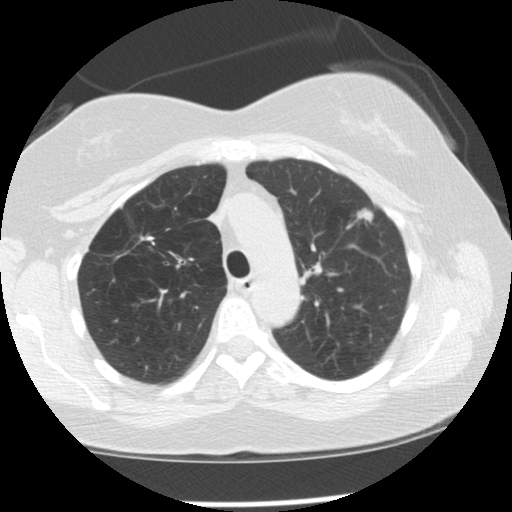
Axial slice from a low-dose chest CT screening exam; second annual screen; lung window (W 1500 / L -600 HU); 2.5 mm slice thickness; slice 37 of 128 in the series; 512 × 512 image matrix, field of view 319 × 319 mm. Female participant, aged 57 years at enrolment.
• Expert-annotated lung lesion, bounding box [x1, y1, x2, y2] px = [345, 202, 384, 237].
• Screening reader's record for this exam (one nodule recorded; not confirmed to be the boxed lesion): non-calcified nodule or mass ≥4 mm, left upper lobe, 11 × 7 mm, spiculated (stellate) margins, soft tissue attenuation, pre-existing on the prior screen: yes; interval growth: yes.